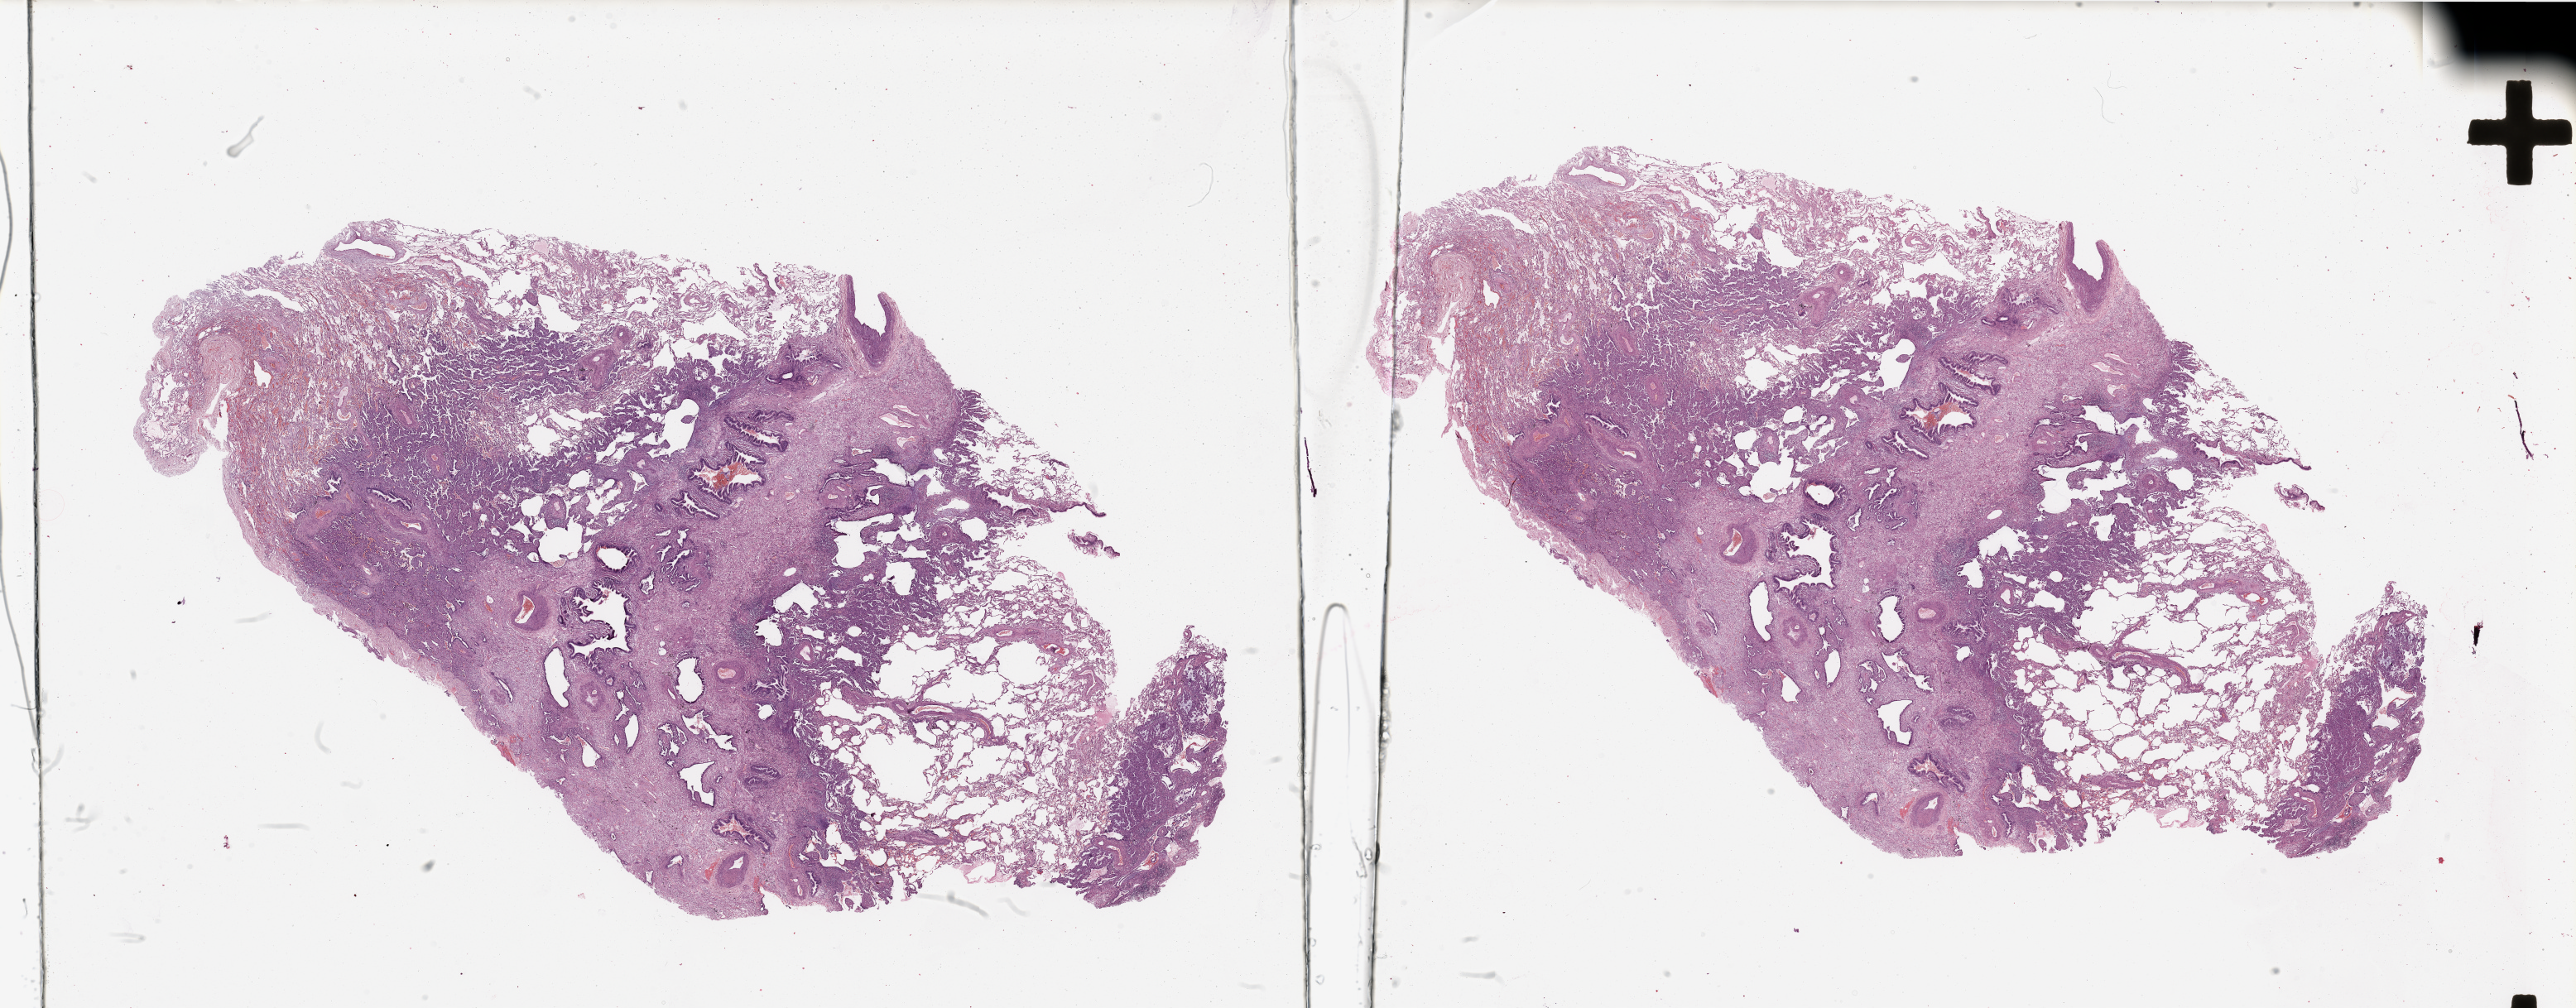
Whole-slide histology image, Hematoxylin and eosin (H&E) stained — whole scanned area (about 49.2 x 19.3 mm, slide scanned at 20x) shown as a low-resolution overview; lung, tumour tissue. Patient: female, age 70 years. Histologic grade: G2 (moderately differentiated).
AJCC pathologic stage: IB. Primary tumour site (as recorded): left lower lobe. Diagnosis: Adenocarcinoma, NOS.